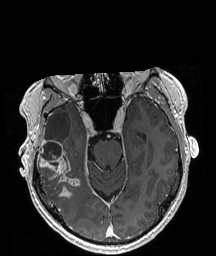
Brain MRI from a brain-tumour surgery series, one axial slice; slice 129 of 208 in the series (ordered by position); T1-weighted post-contrast; 1 mm slice thickness; 216 × 256 image matrix, field of view 211 × 250 mm. From the clinical record (not read from this slice): histopathology: Astrocytoma; WHO grade: 4; IDH mutation: yes.
Outlined on this slice (outlined manually by an expert reader):
- tumour: bounding box [x1, y1, x2, y2] px = [37, 141, 80, 197]